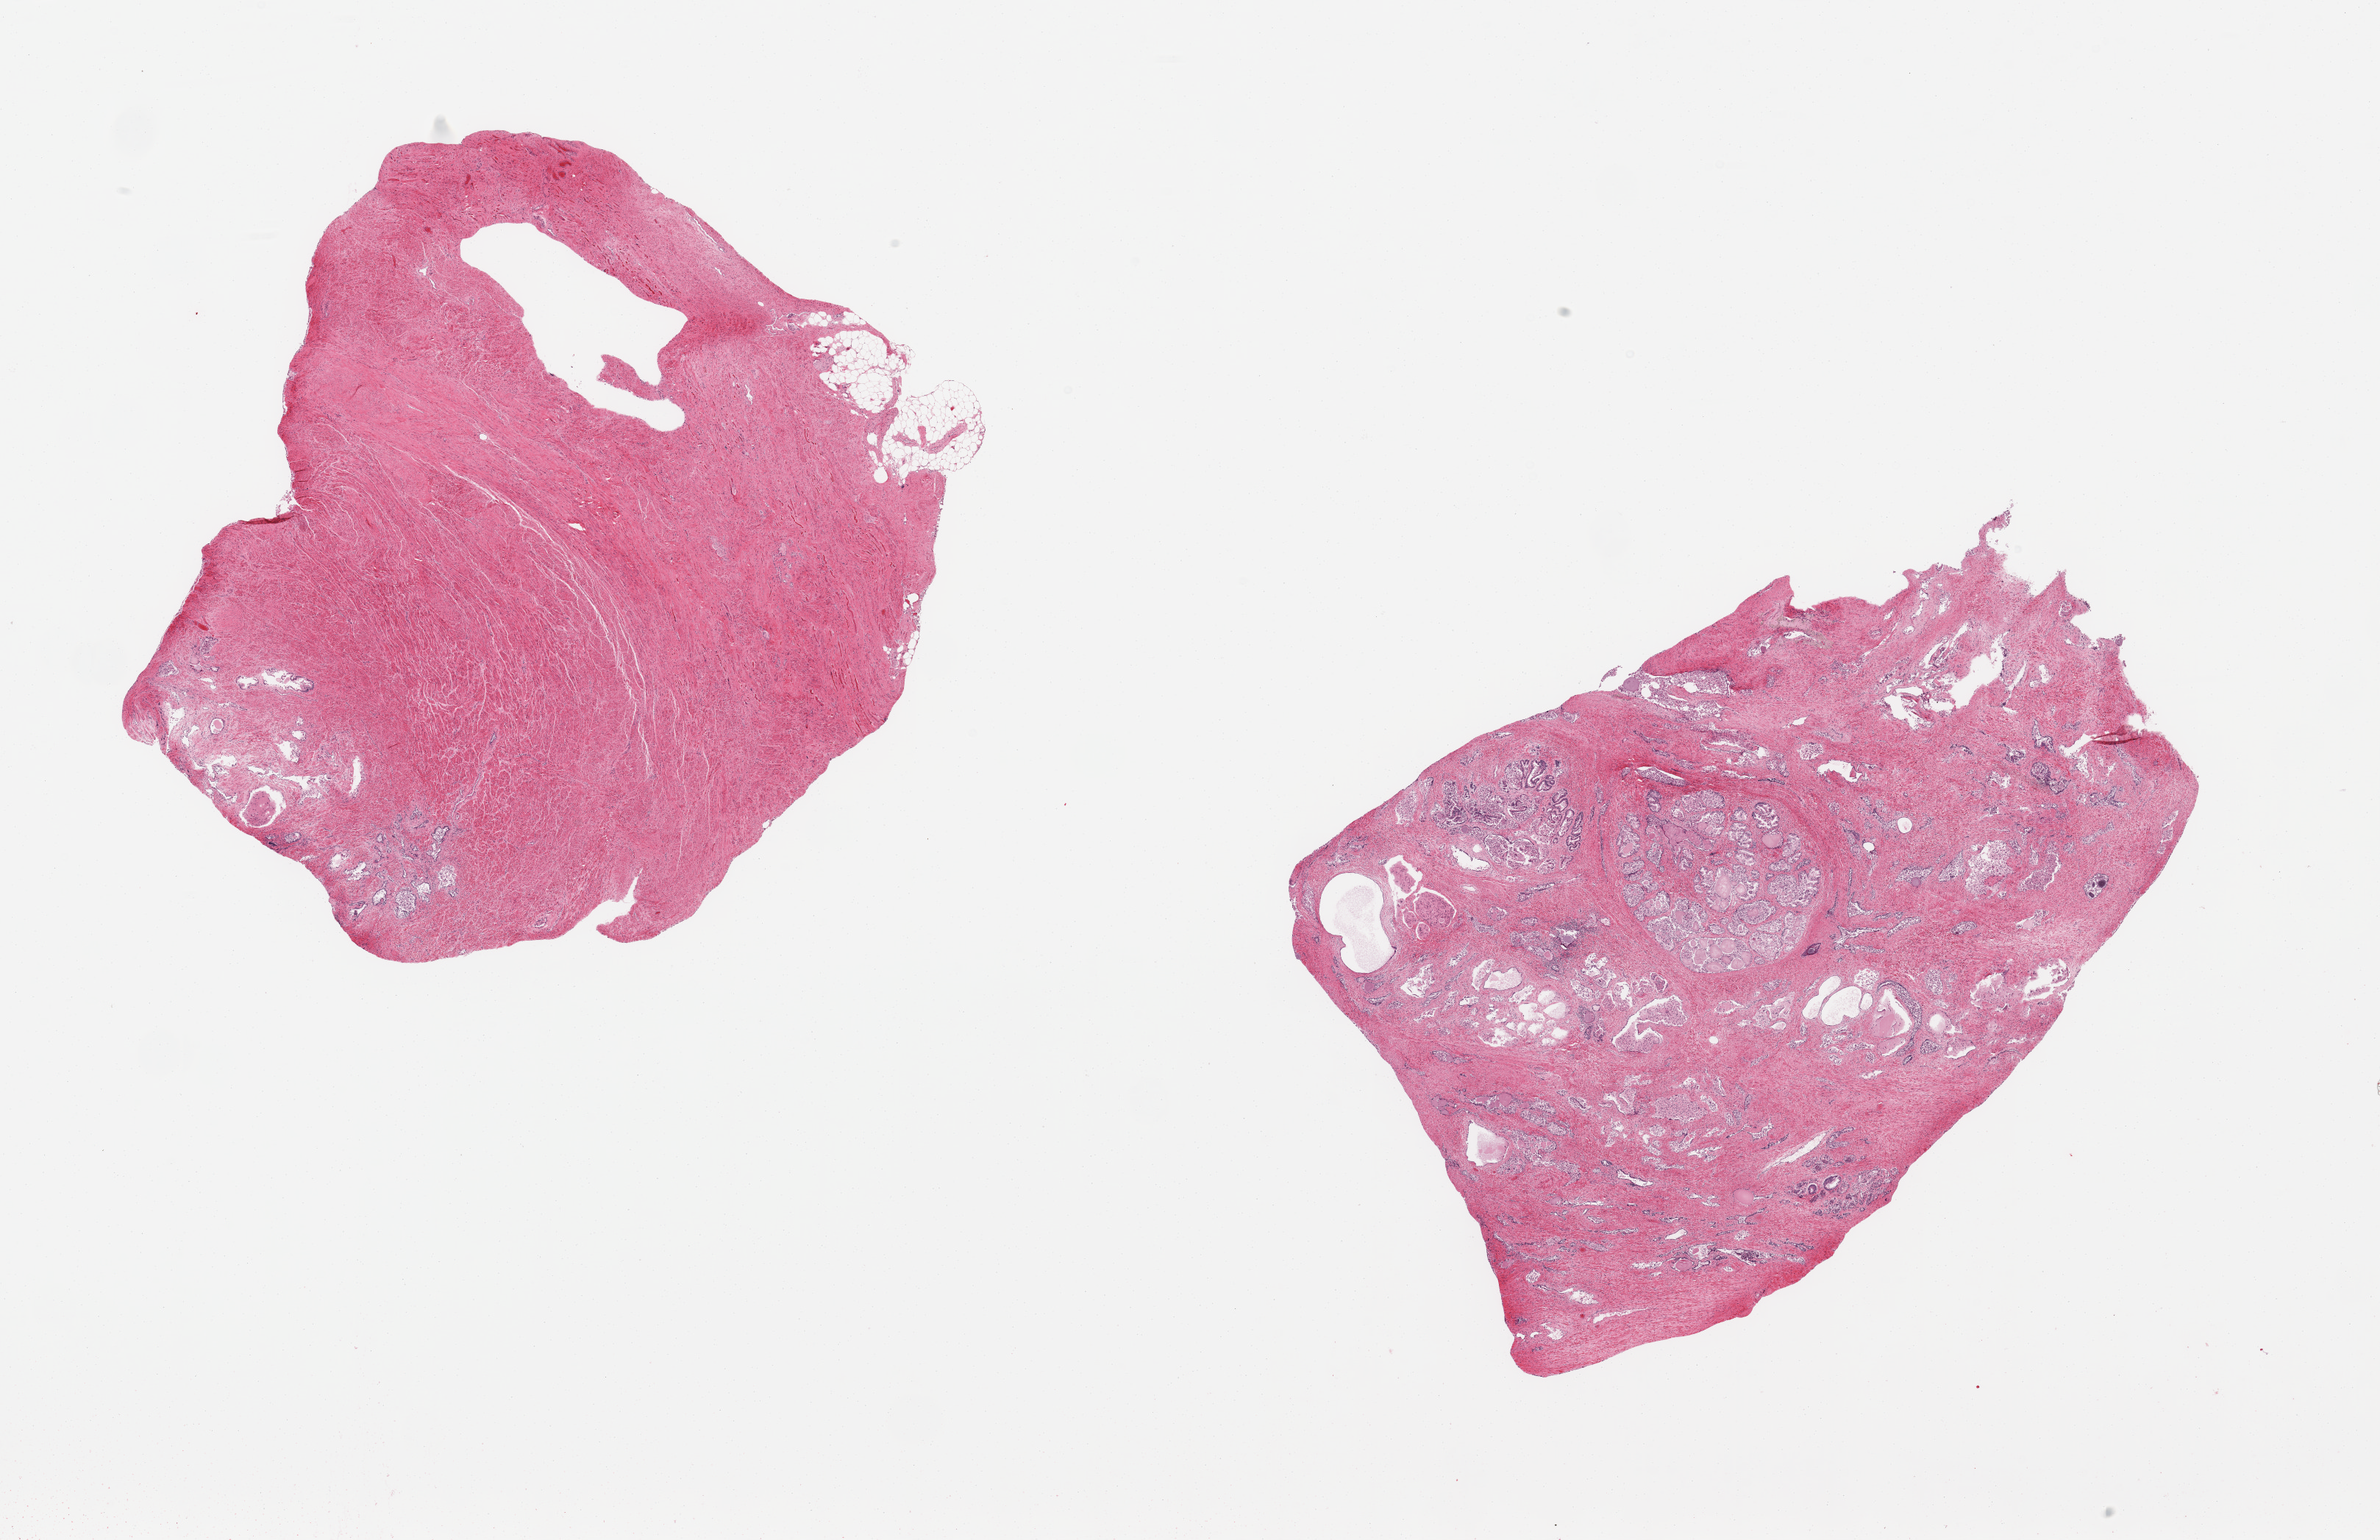
H&E whole-slide image, shown as a low-resolution overview of the whole scanned area (about 25.6 x 16.6 mm, from a 20x scan), PAXgene-fixed, paraffin-embedded tissue, sampled site (target tissue): prostate, donor tissue sample. Donor: male.
Pathologist's review note for this sample: 2 pieces; 1 piece has 60% glands which are totally autolyzed; other is largely intact smooth muscle stroma with 10% autolyzed glands.